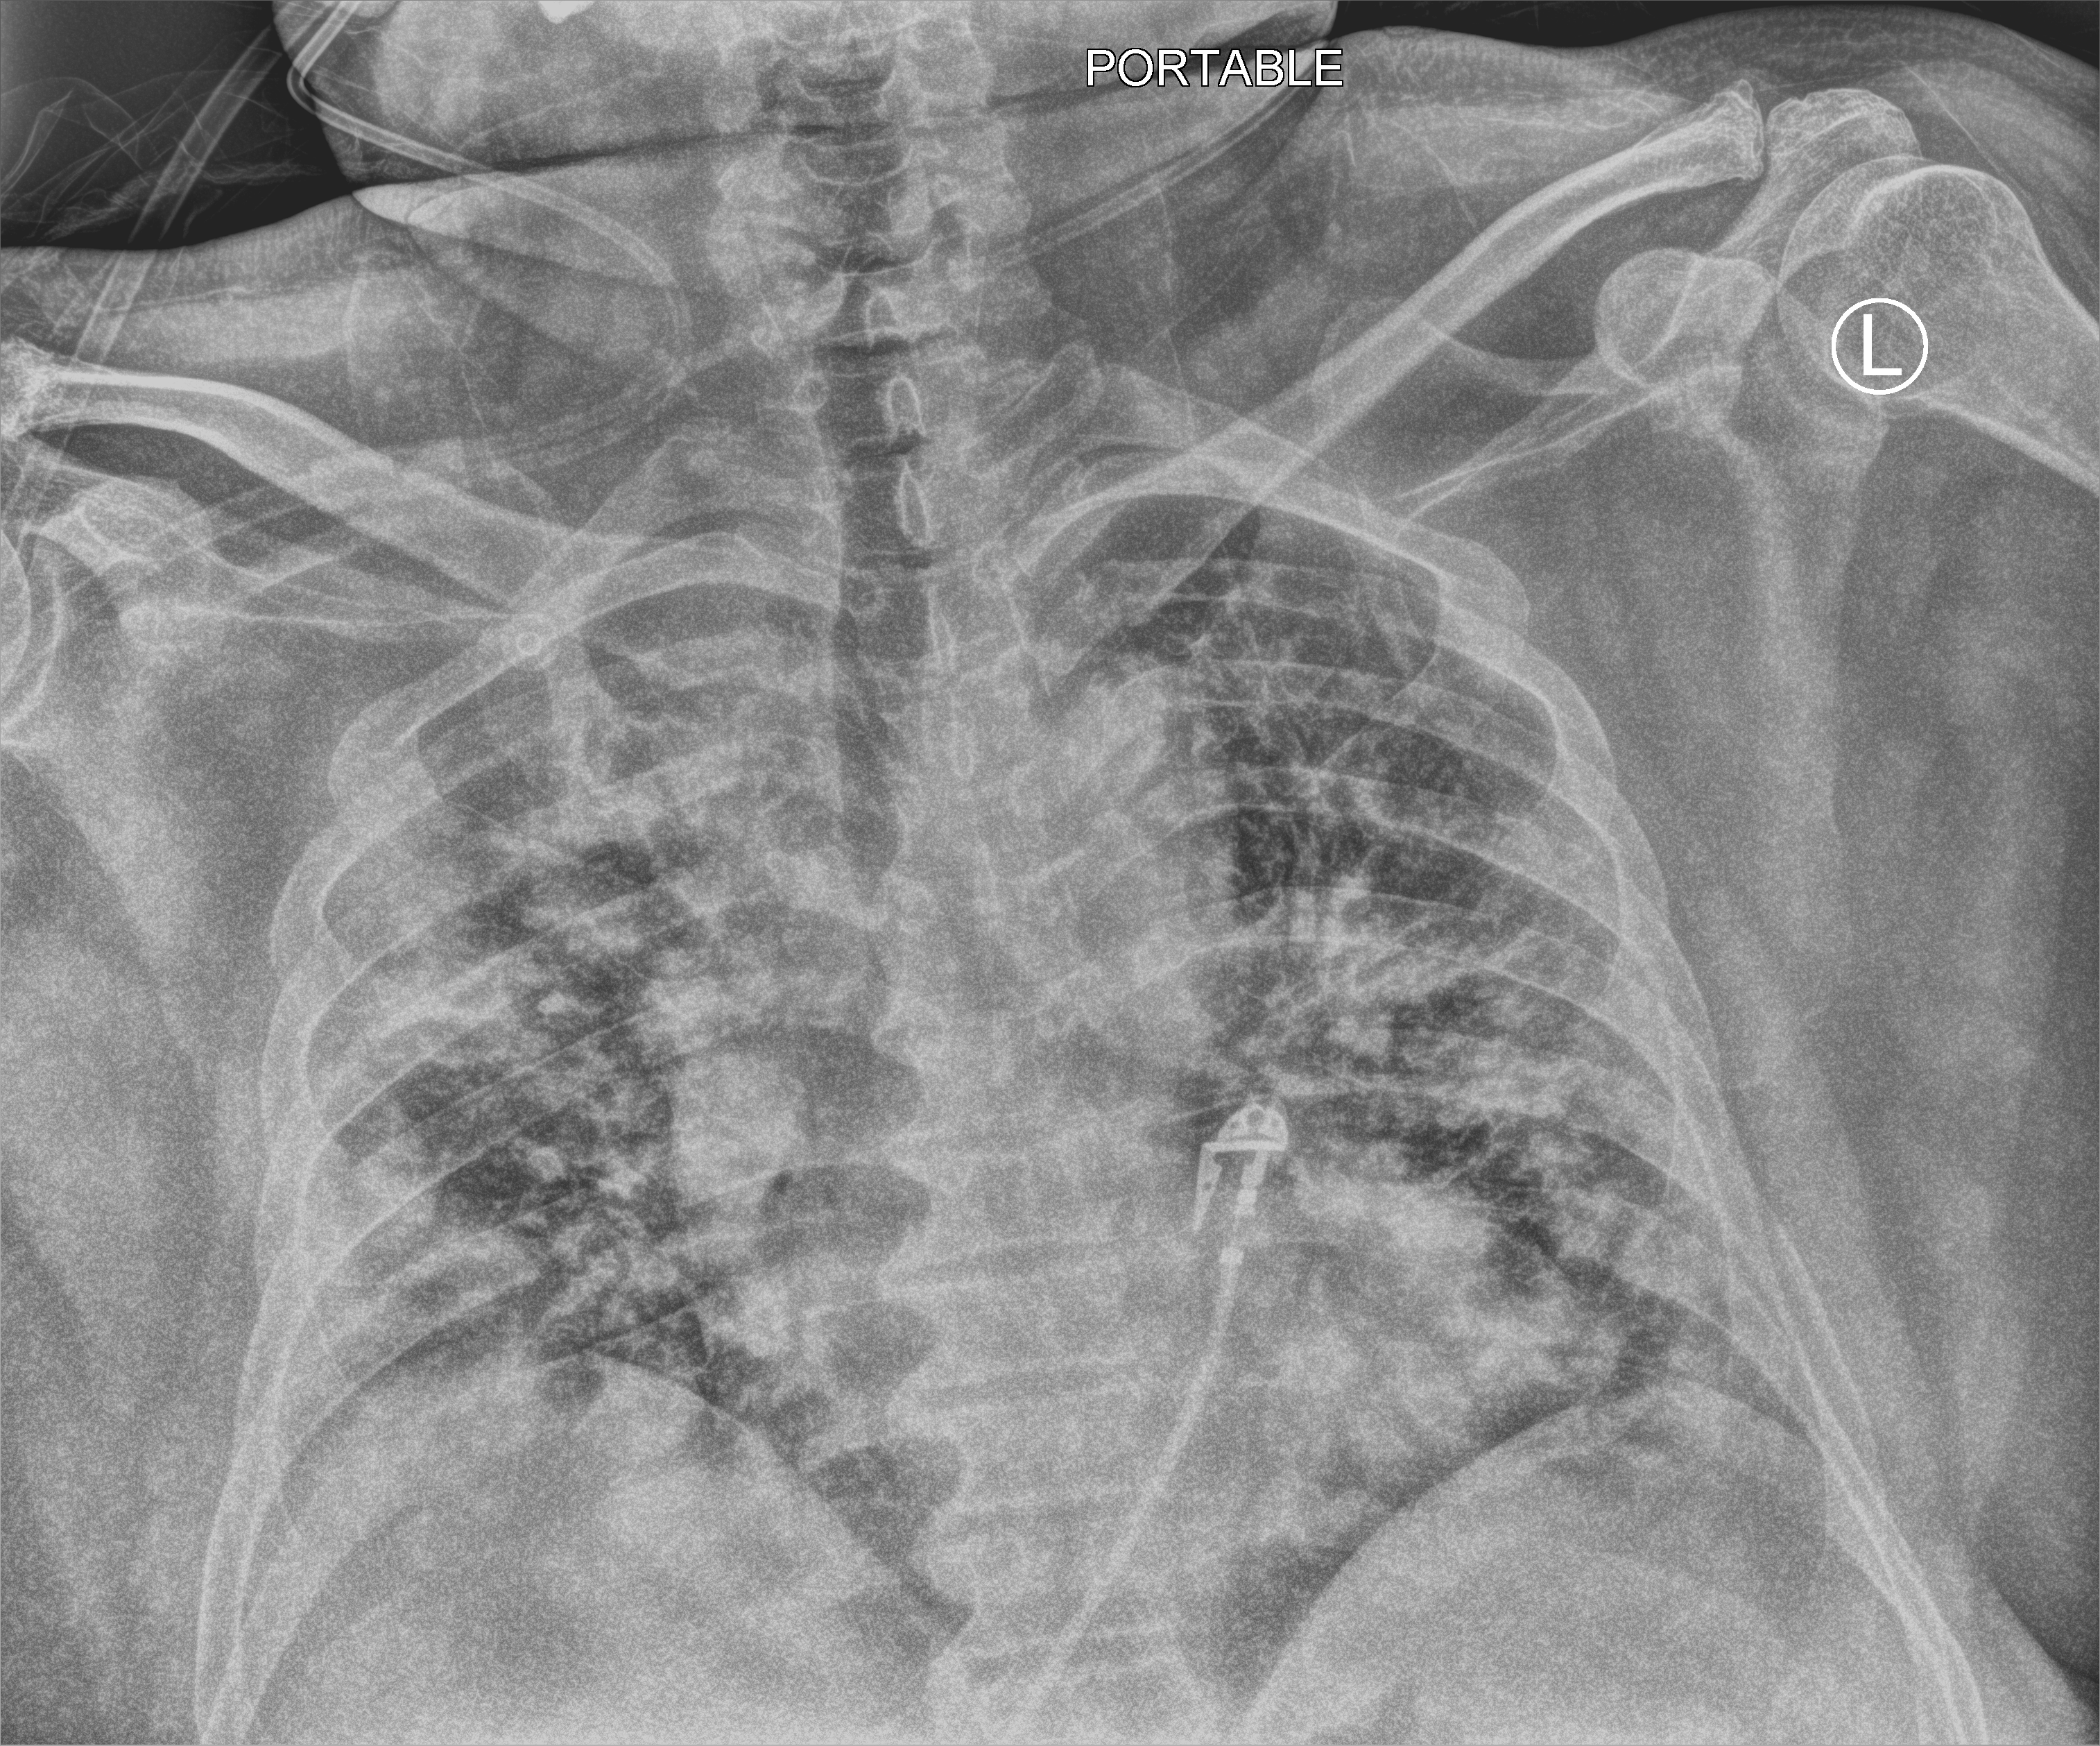
Bedside chest radiograph (computed radiography); anteroposterior (AP) projection. Adult patient hospitalised with COVID-19, age 18–59 years.
From the hospital-stay record, not from the radiograph (when in the stay this image was taken is not recorded):
- hypertension (admission record): yes